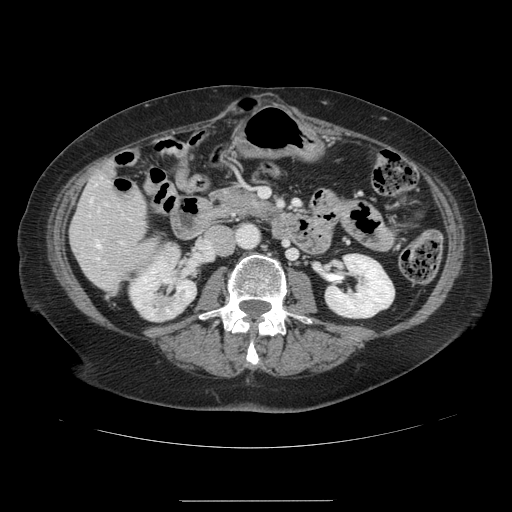
Contrast-enhanced abdominal CT, one axial slice. 120 kVp. Intravenous contrast given. Soft-tissue window (W 400 / L 40 HU). 2.5 mm slice thickness. 512 × 512 image matrix, field of view 393 × 393 mm. Female patient, age 74 years. From the clinical record (not read from this slice): diagnosis: colorectal cancer liver metastases, imaged before liver resection; multiple liver metastases: yes; largest metastasis: 7 cm.
Structures marked on this image (outlined manually by an expert reader):
- hepatic veins: bounding box <90,199,99,247> (left, top, right, bottom; pixels)
- liver: <71,173,155,291>
- planned liver remnant (the part of the liver to remain after resection): <71,173,155,288>
- portal vein (with intrahepatic branches): <106,203,122,243>